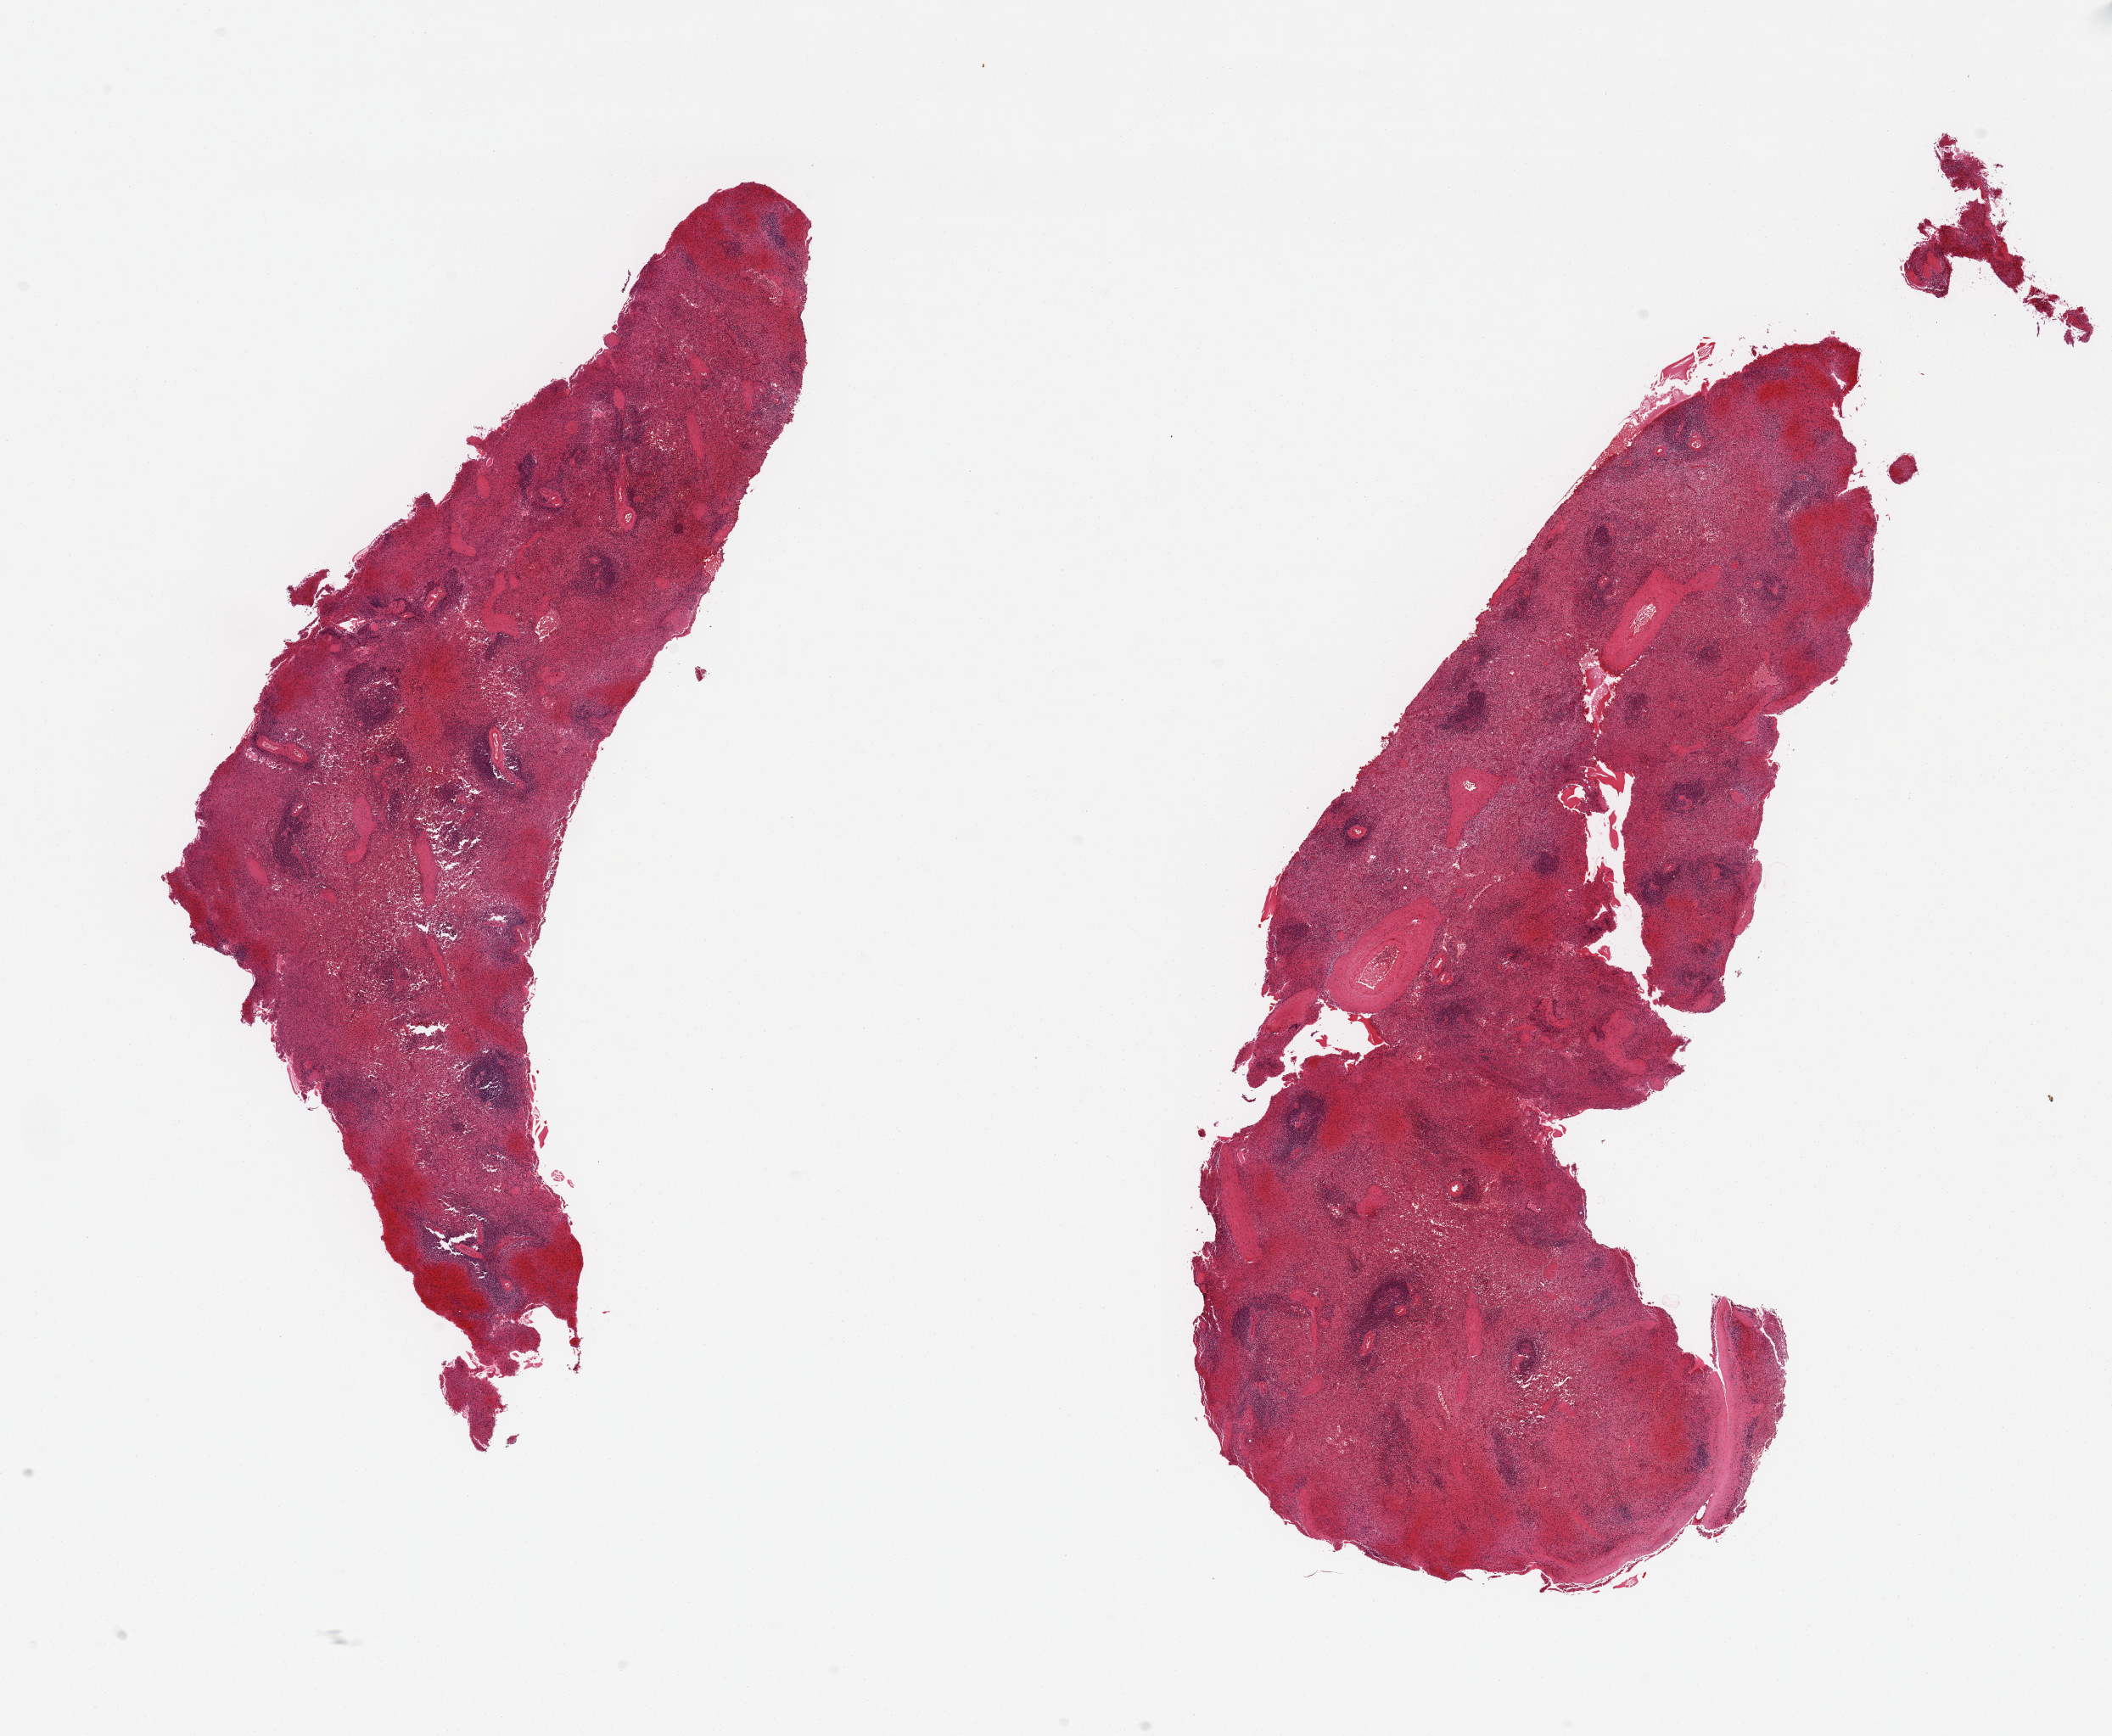
Whole-slide image, H&E stain, whole scanned area (about 19.7 x 16.2 mm, from a 20x scan) shown as a low-resolution overview. PAXgene-fixed paraffin-embedded (PFPE) section. Sampled site (target tissue): spleen. Donor tissue sample. Donor: male.
Pathologist's review note for this sample: 2 pieces, marked congestion.